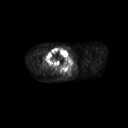
FDG PET of an extremity soft-tissue mass (from a PET/CT study), one axial slice; slice 260 of 311 in the series (ordered by position); 3.27 mm slice thickness; 128 × 128 image matrix. Male patient, age 50 years. Case-level facts recorded for this patient, not image findings: histological type: undifferentiated - pleiomorphic; grade: high; site of the primary tumour: right thigh.
Annotated regions visible in this slice (expert contour drawn on MRI and transferred to this co-registered scan by the dataset authors):
- gross tumour volume including surrounding oedema: bounding box (x1, y1, x2, y2) in pixels: (43, 47, 66, 68)
- gross tumour volume (mass): (45, 48, 66, 68)